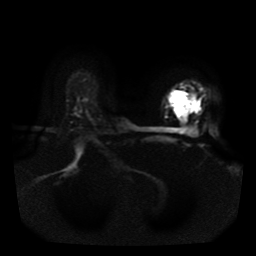
Breast MRI, one axial slice. Position 31 of 41 along the scan axis. Diffusion-weighted series; image 2 of 4 stored at this slice position (different b-values; order by instance number). 1.5 T. 5 mm slice thickness. 256 × 256 image matrix, field of view 330 × 330 mm. Female patient.
Structures marked on this image (manually delineated by an expert):
- tumour on diffusion-weighted imaging: bounding box (x1, y1, x2, y2) in pixels: (170, 93, 197, 118)